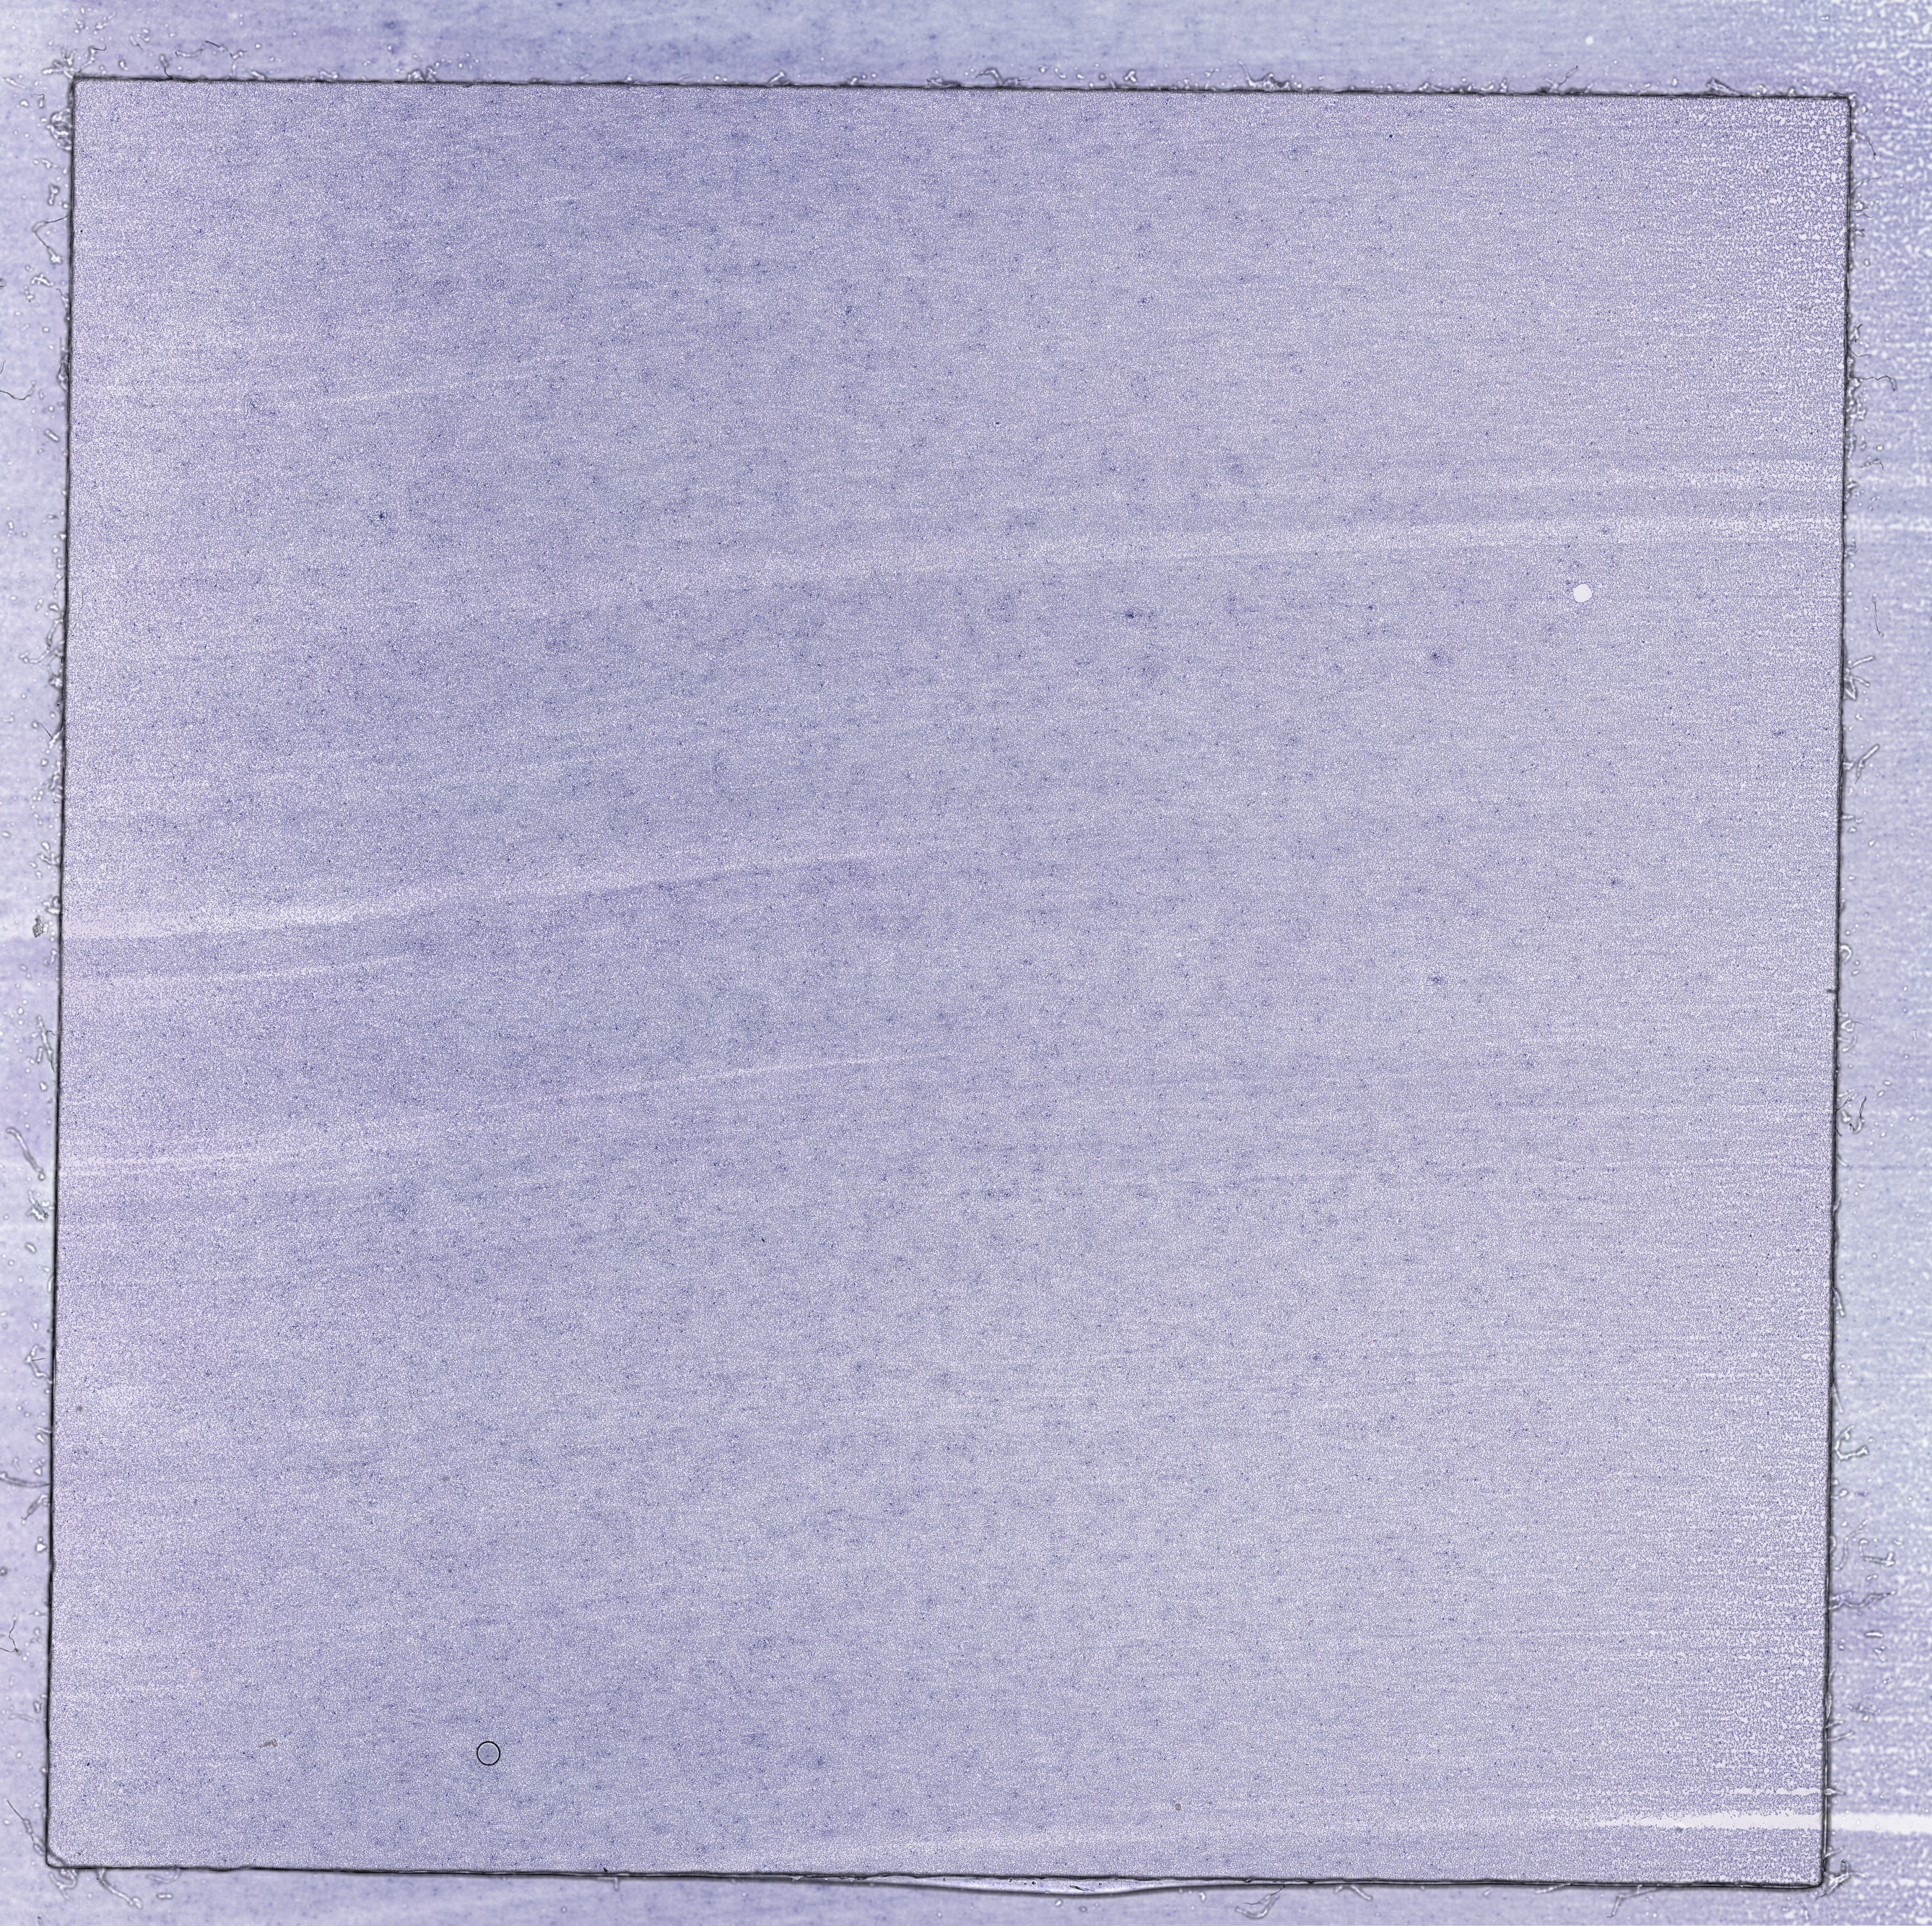
Digitized H&E-stained tissue section (whole slide) — a low-resolution overview of the entire scanned area, about 21.6 x 21.5 mm; peripheral blood (leukaemic) sample. 73-year-old male patient.
Diagnosis: Acute Myeloid Leukemia. WHO classification: AML with maturation. FAB classification: M2.